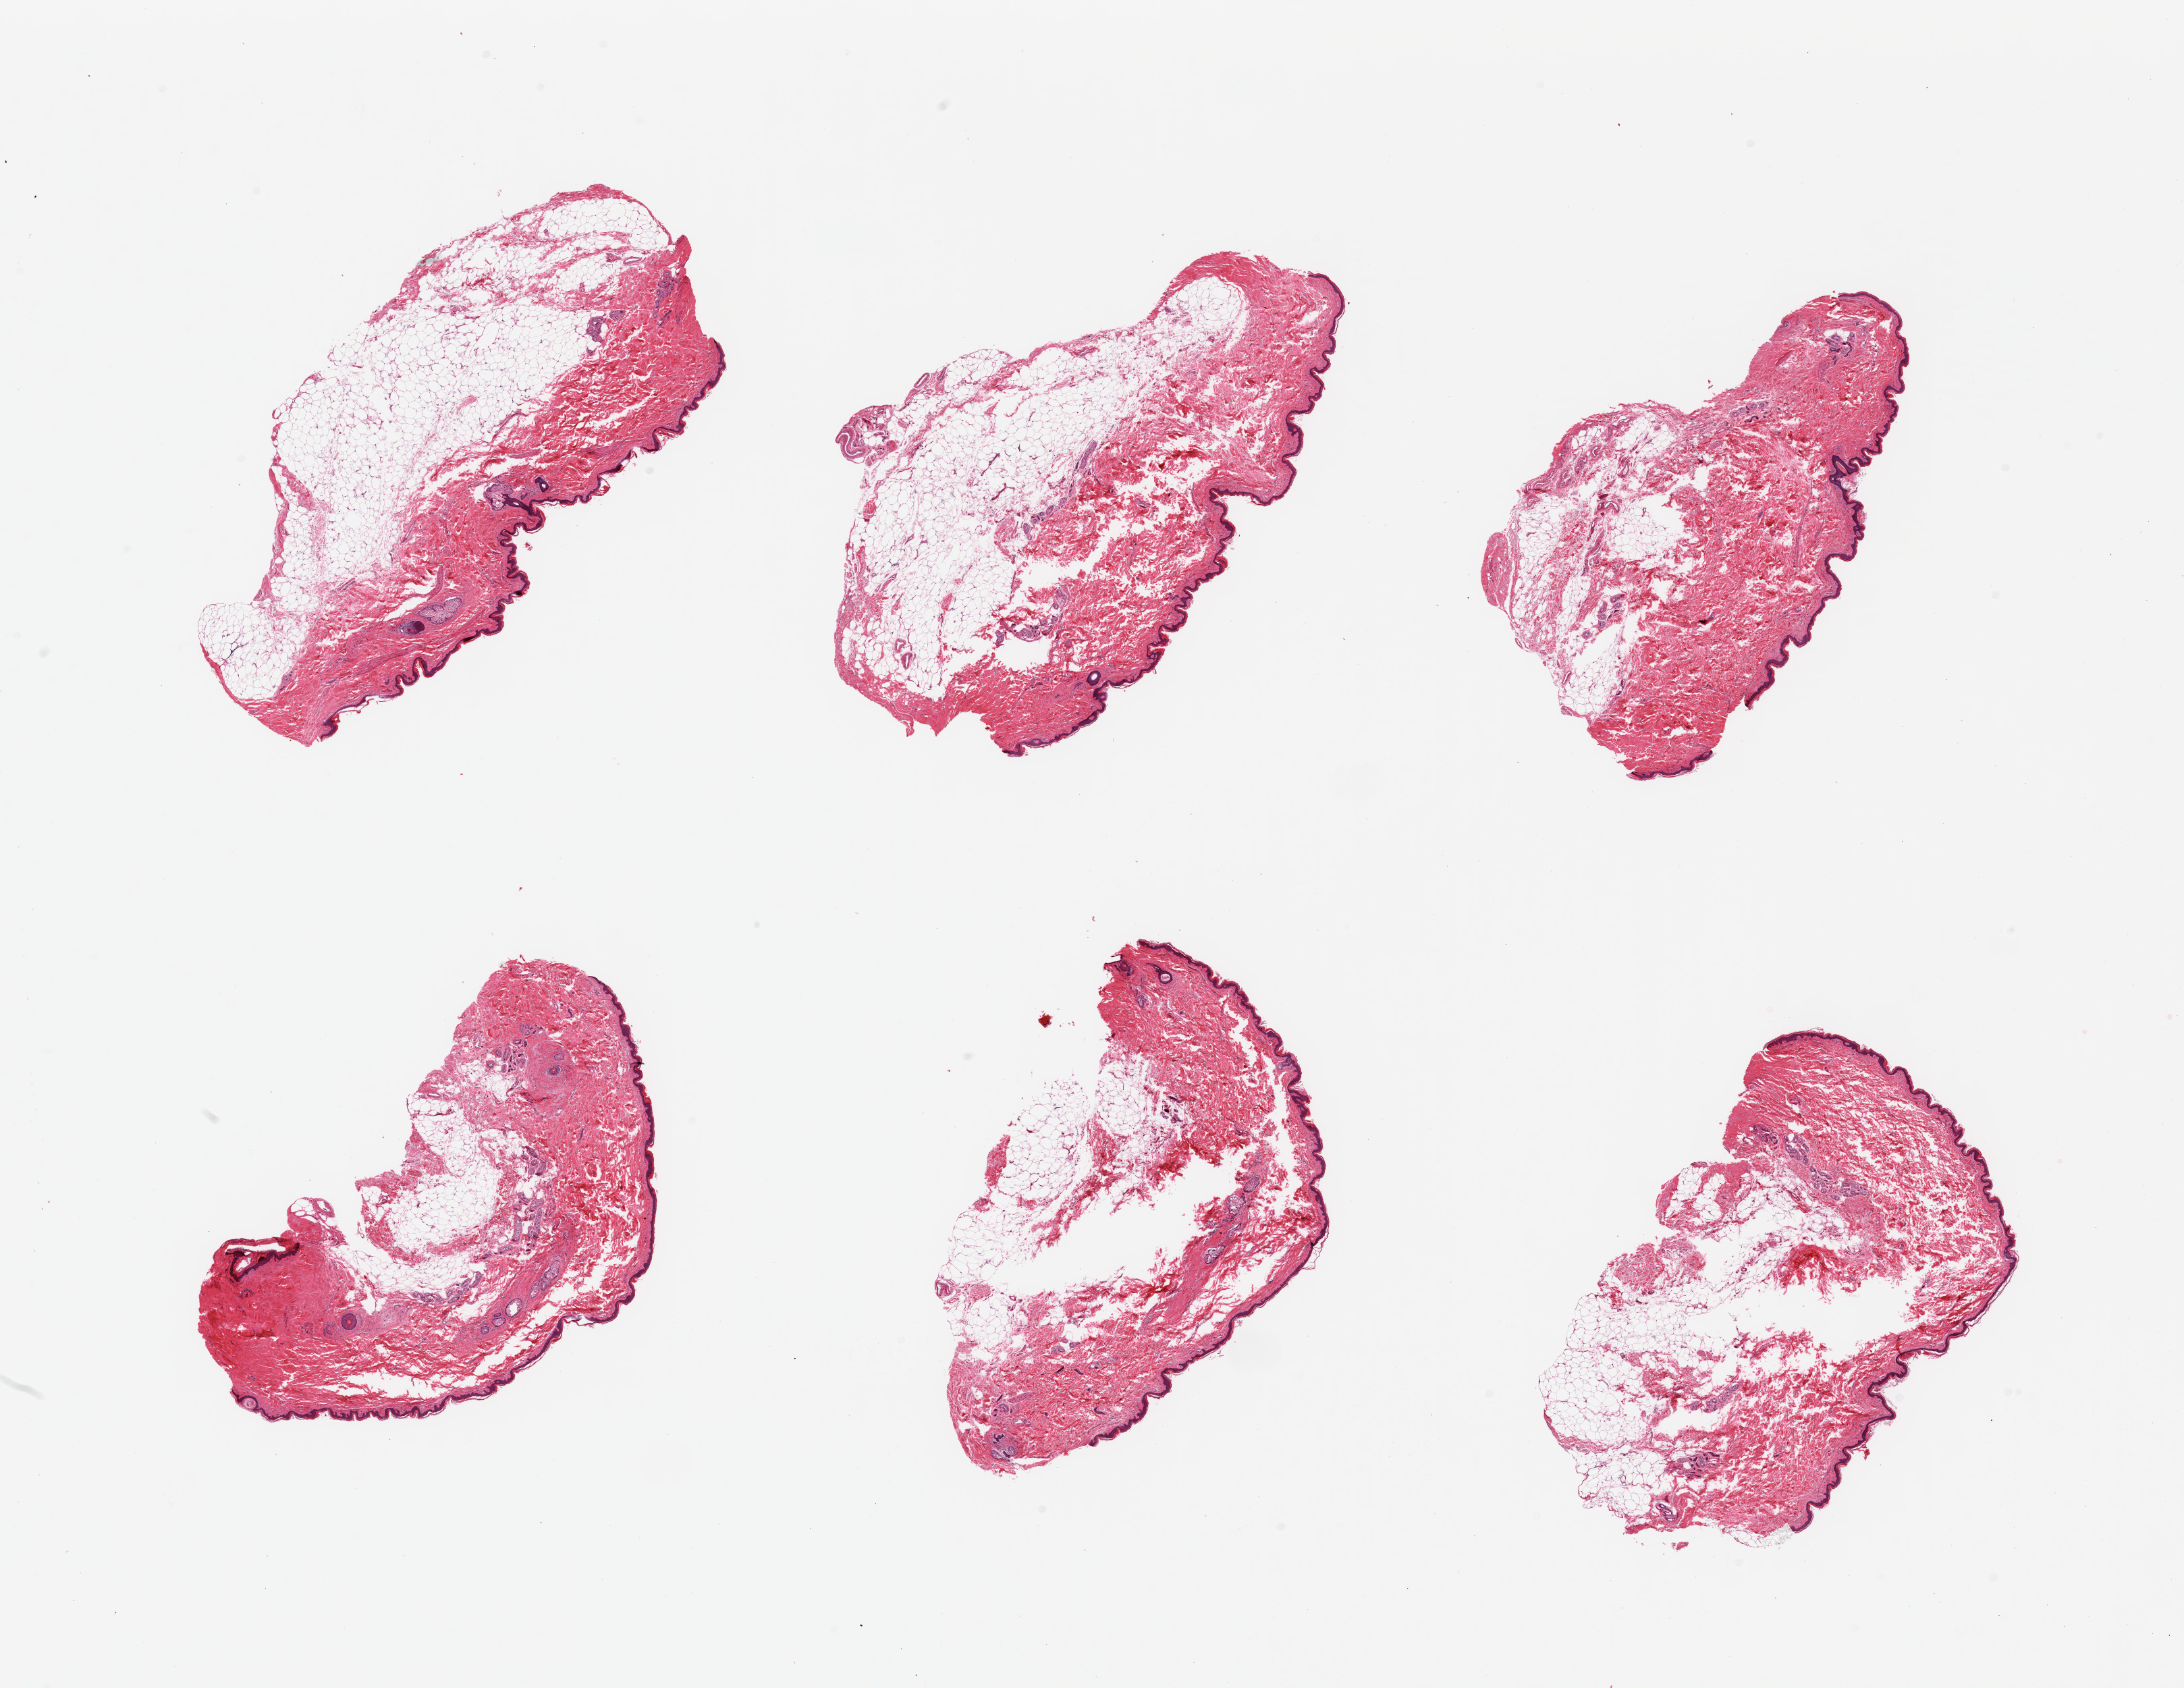
Whole-slide image, hematoxylin and eosin (H&E) stain — low-resolution overview of the scanned area, about 25.6 x 19.8 mm. PAXgene-fixed, paraffin-embedded tissue. Section of skin of suprapubic region (target tissue). Tissue donor sample. Donor: female.
Review note (as recorded): 6 pieces; up to 60% subcutaneous fat.